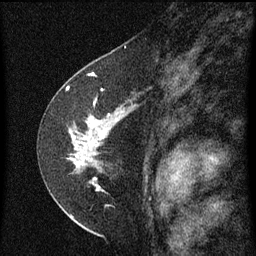
Breast MRI (dynamic contrast-enhanced), one sagittal slice; slice 38 of 60 in the series (ordered by position); dynamic contrast-enhanced series, image 2 of 3 at this slice position (ordered by acquisition); 1.5 T; TE 4.2 ms, TR 8 ms; 2 mm slice thickness; 256 × 256 image matrix, field of view 180 × 180 mm. Patient: female, 47 years.
Structures marked on this image (semi-automatic segmentation, software-assisted and operator-edited):
- analysis volume of interest (the breast-tissue region the enhancement analysis was run in; not a lesion): bounding box (x1, y1, x2, y2) in pixels: (46, 84, 137, 199)
- tumour enhancement mask (voxels above the 70 % enhancement threshold inside the analysis volume of interest): (72, 112, 125, 191)